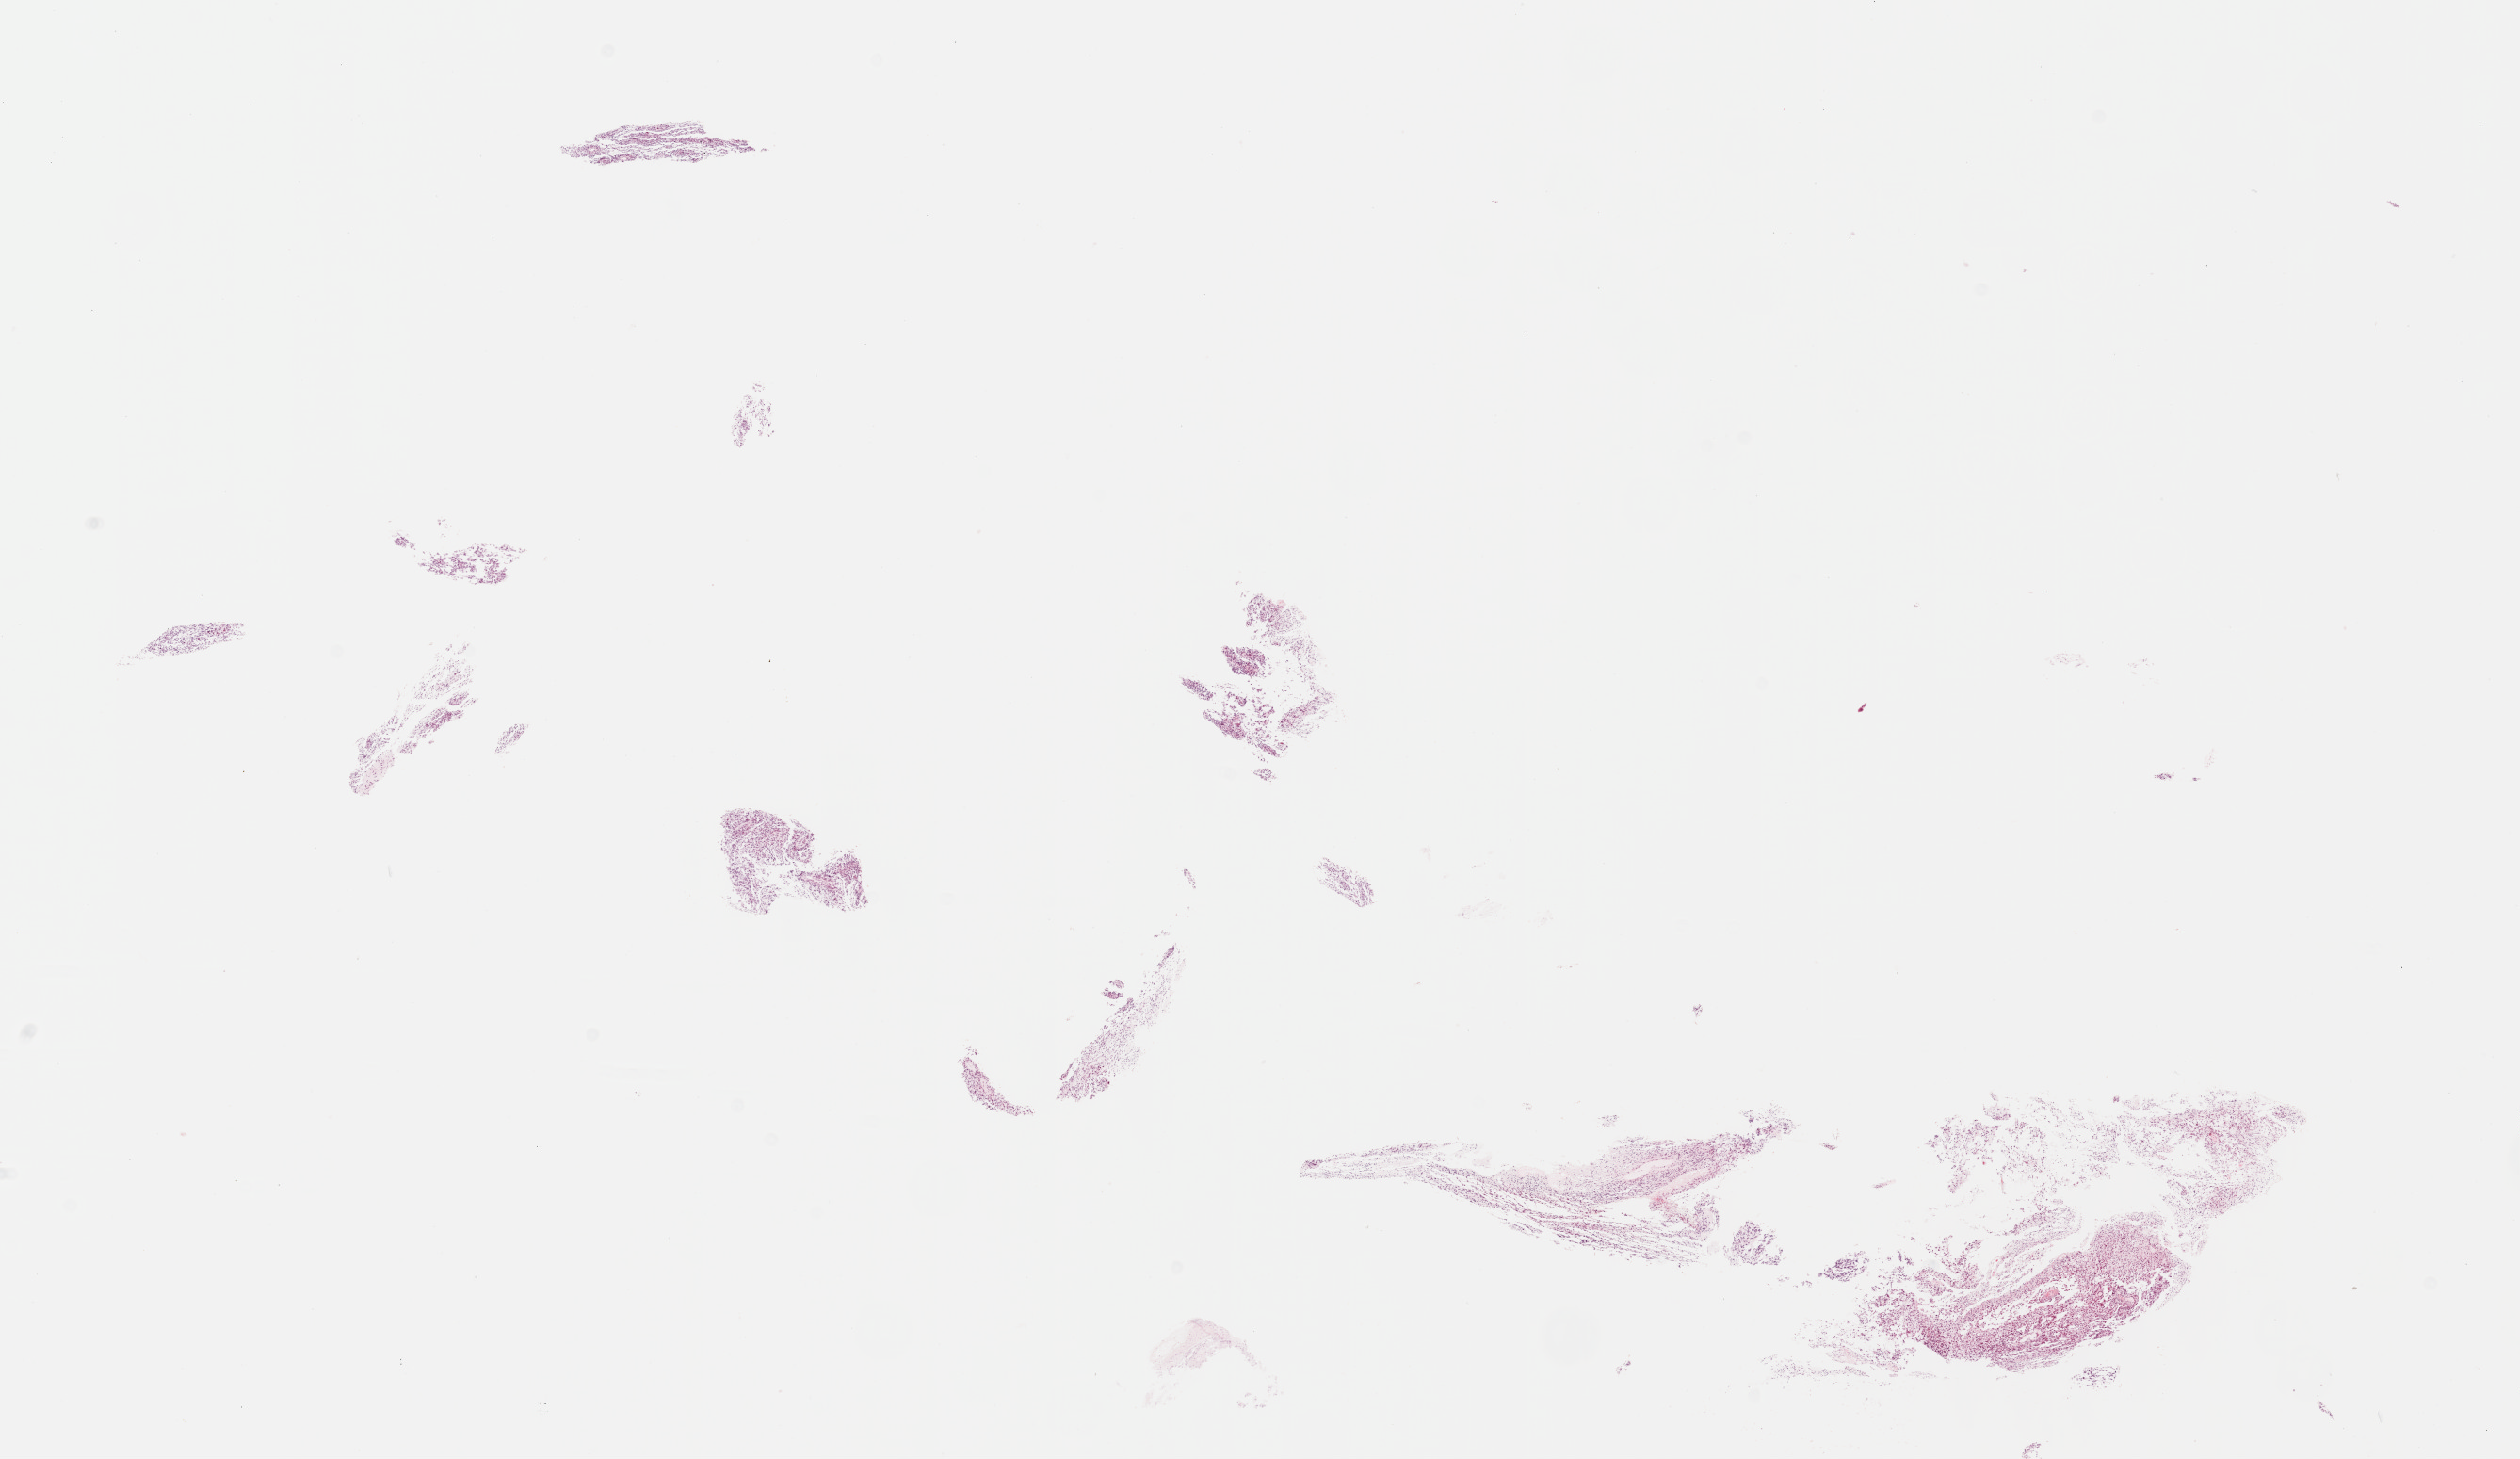
H&E whole-slide image, shown as a low-resolution overview of the whole scanned area (about 21.6 x 12.5 mm, from a 40x scan), FFPE section, primary tumour sample from the brain. Male, age 69 years at initial diagnosis.
Pathologic diagnosis: Glioblastoma.